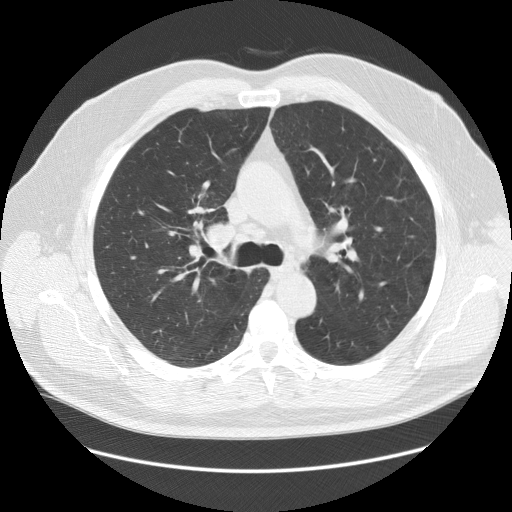
Chest CT (low-dose screening protocol), one axial image. Baseline screening round. Lung window (W 1500 / L -600 HU). Standard (soft-tissue) reconstruction kernel (STANDARD). Slice 48 of 140 in the series. Male, age 64 years at enrolment.
Expert reader's lesion annotation, bounding box <179,208,252,274> (left, top, right, bottom; pixels). Screening reader's record for this exam (one nodule recorded; not confirmed to be the boxed lesion): non-calcified nodule or mass ≥4 mm, right lower lobe, 7 × 5 mm, smooth margins, soft tissue attenuation. Official screen result: positive, change unspecified: nodule(s) >= 4 mm or enlarging nodule(s), mass(es), or other non-specific abnormalities suspicious for lung cancer. Lung cancer was diagnosed 456 days after this screen: adenocarcinoma, NOS, right upper lobe, poorly differentiated (G3), stage IB (AJCC 6th edition), 37 mm at pathology.